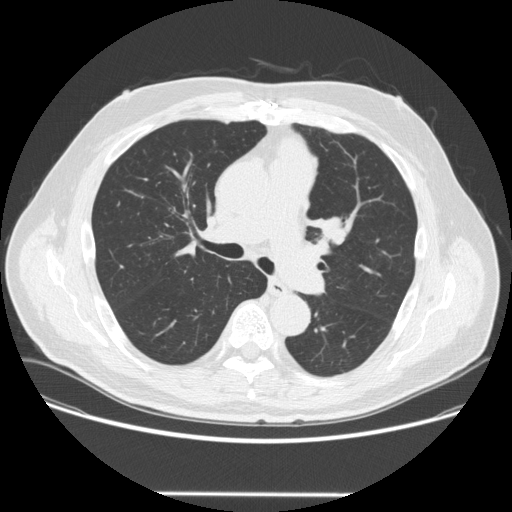
Low-dose screening chest CT, one axial slice; slice 163 of 253 in the series (ordered by position); reconstruction kernel STANDARD; lung window (W 1500 / L -600 HU); 2.5 mm slice thickness; 512 × 512 image matrix, field of view 400 × 400 mm.
Outlined on this slice (outlined manually by an expert reader):
- lesion 1 (tumor, upper lobe of left lung): box from (x=318, y=219) to (x=343, y=243) px